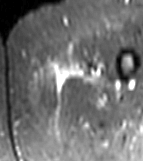
MRI of an extremity soft-tissue mass, one axial slice. STIR. MR volume resampled by the dataset authors to the PET/CT grid (not the native acquisition matrix). 3.27 mm slice thickness. 143 × 161 image matrix. Female patient. Case-level facts recorded for this patient, not image findings: histological type: myxofibrosarcoma; grade: intermediate; site of the primary tumour: left thigh.
Structures marked on this image (expert contour drawn on MRI and transferred to this co-registered scan by the dataset authors):
- gross tumour volume including surrounding oedema: bounding box [x1, y1, x2, y2] px = [49, 60, 107, 89]